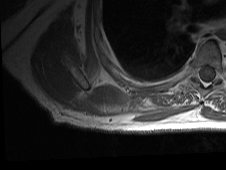
MRI of an extremity soft-tissue mass, one axial slice; slice 15 of 81 in the series (ordered by position); MR volume resampled by the dataset authors to the PET/CT grid (not the native acquisition matrix); 3.27 mm slice thickness; 226 × 170 image matrix, field of view 221 × 166 mm. Male patient. Case-level facts recorded for this patient, not image findings: histological type: pleiomorphic spindle cell undifferentiated; grade: high; site of the primary tumour: right parascapusular.
Structures marked on this image (expert contour drawn on MRI and transferred to this co-registered scan by the dataset authors):
- gross tumour volume including surrounding oedema: bounding box <124,100,189,121> (left, top, right, bottom; pixels)